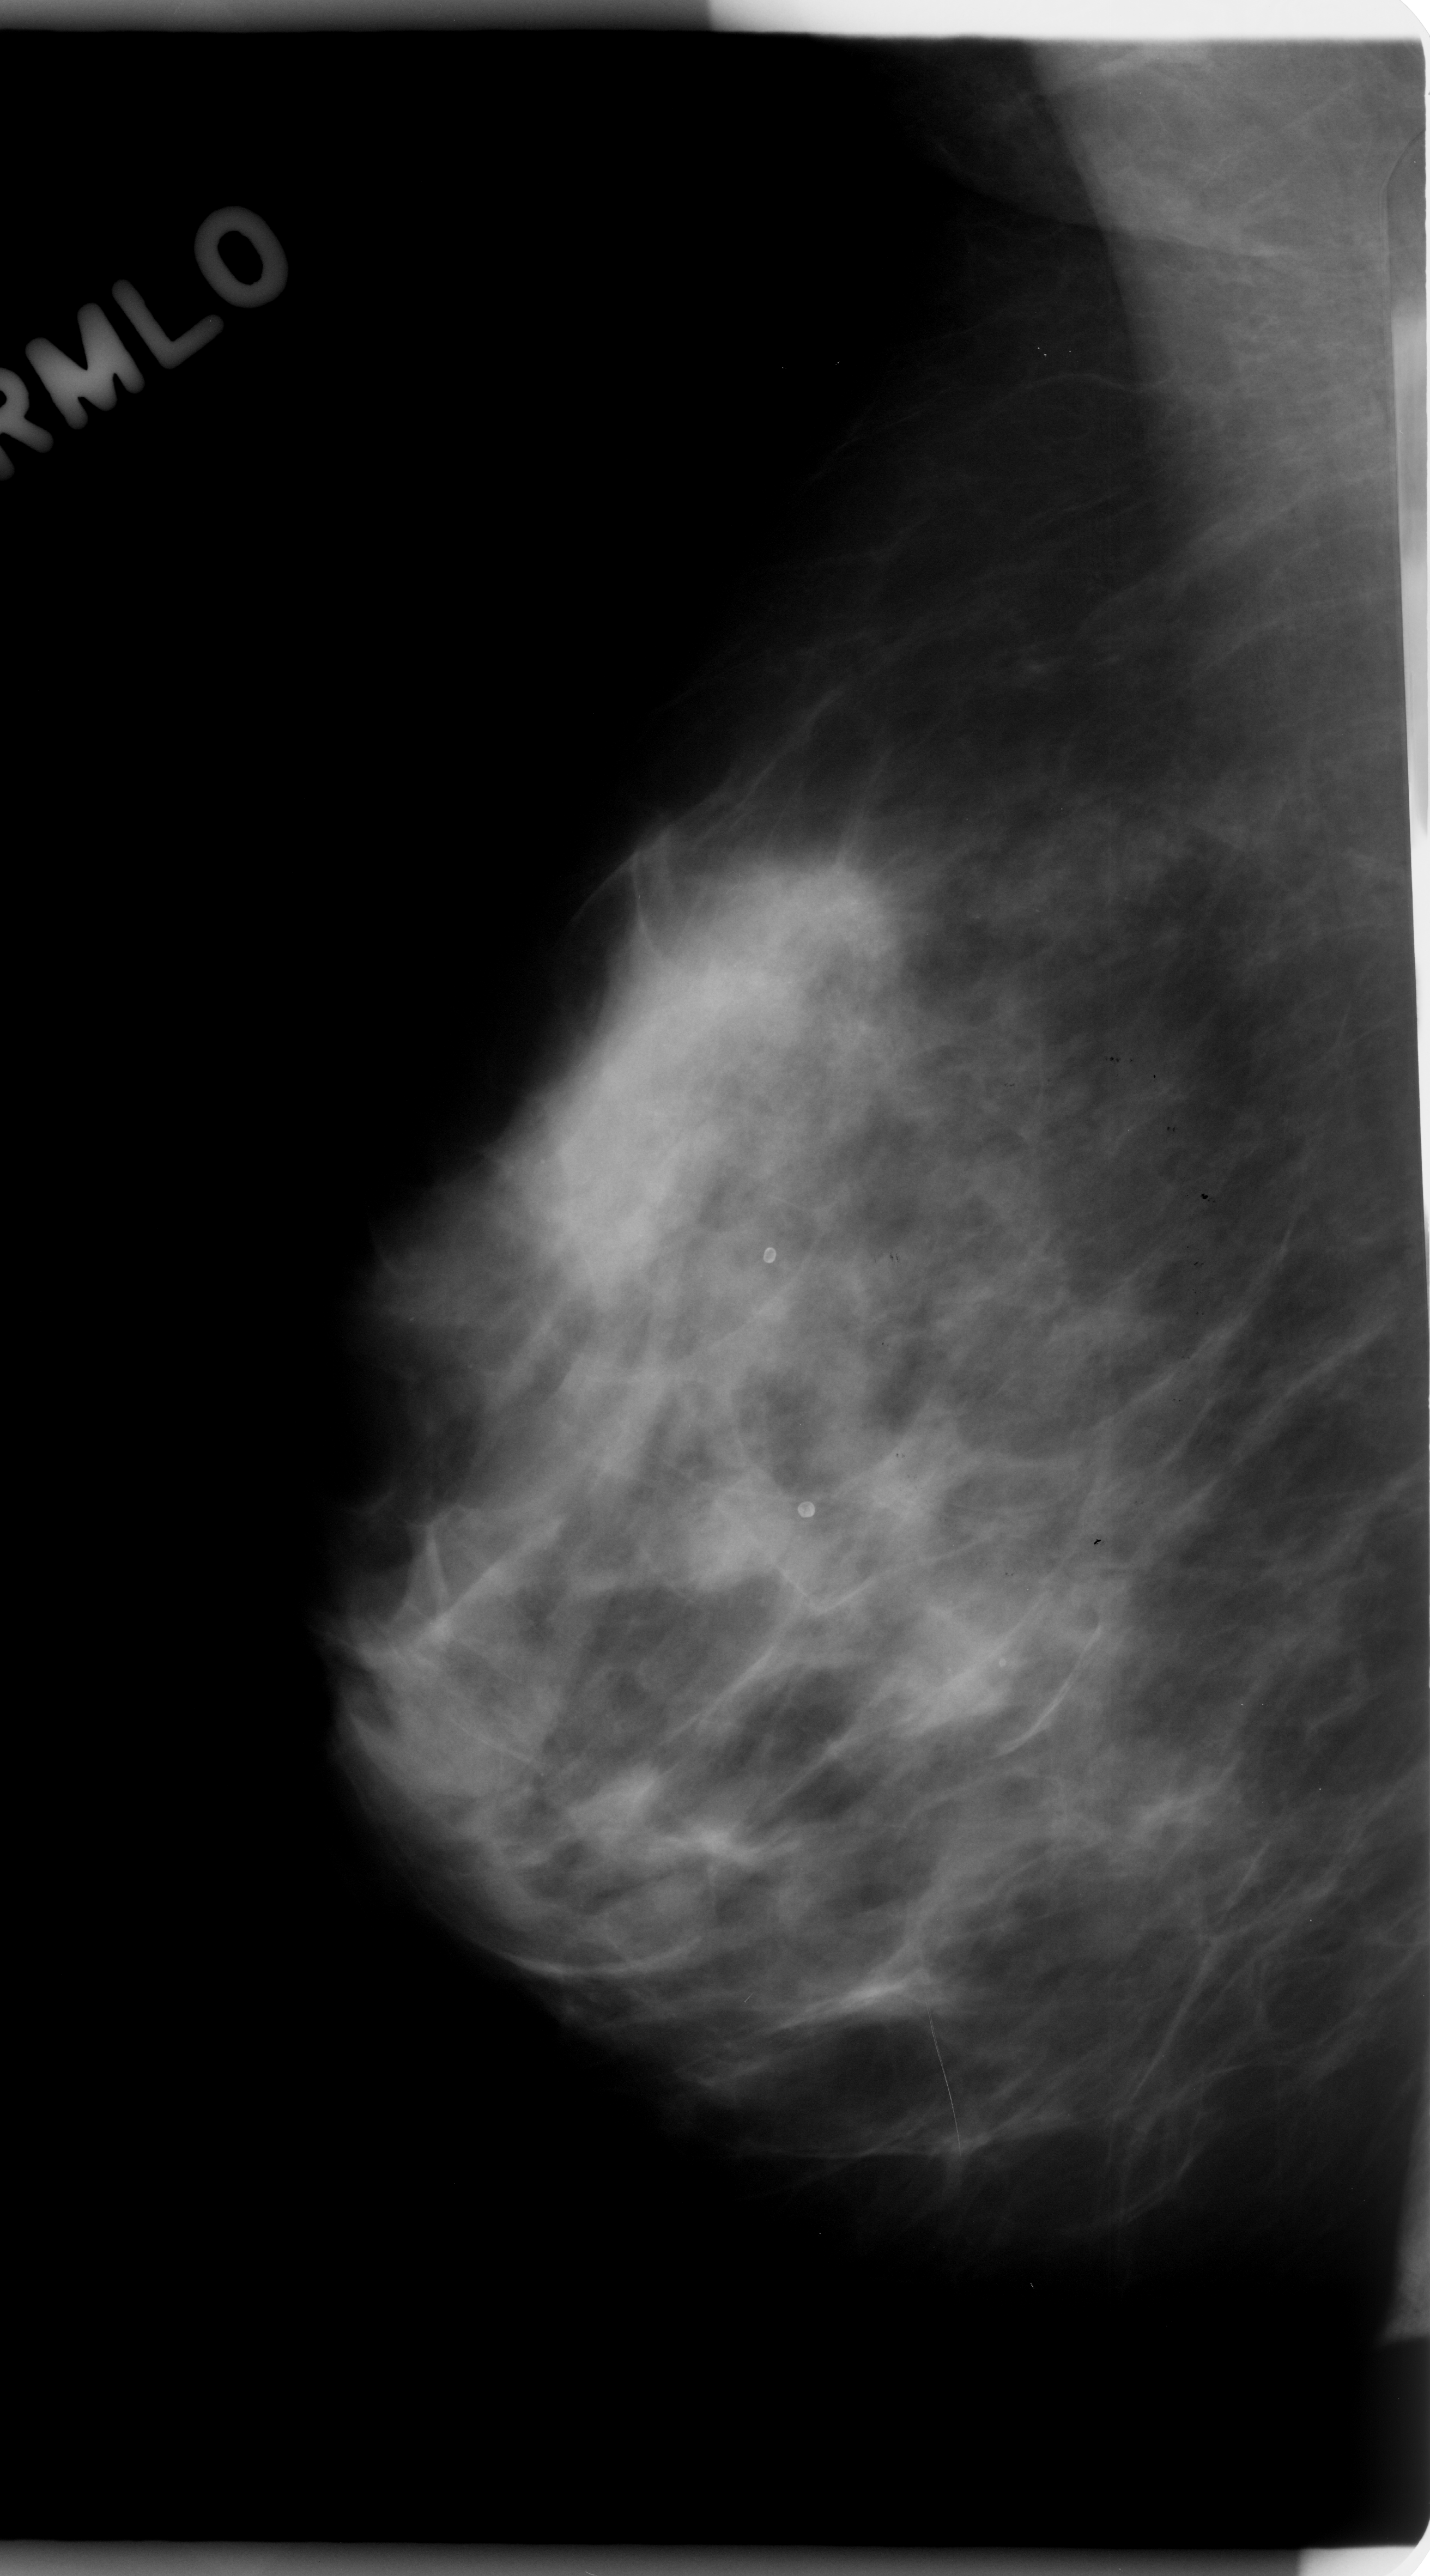
Scanned film-screen mammogram; right breast; mediolateral oblique (MLO) view; breast composition: heterogeneously dense (BI-RADS density category 3 of 4).
- Finding: calcifications, morphology amorphous, distribution clustered; BI-RADS assessment category 5; subtlety rating 5 on a 1 (subtle) to 5 (obvious) scale; pathology result (as recorded, not read from the image): malignant.